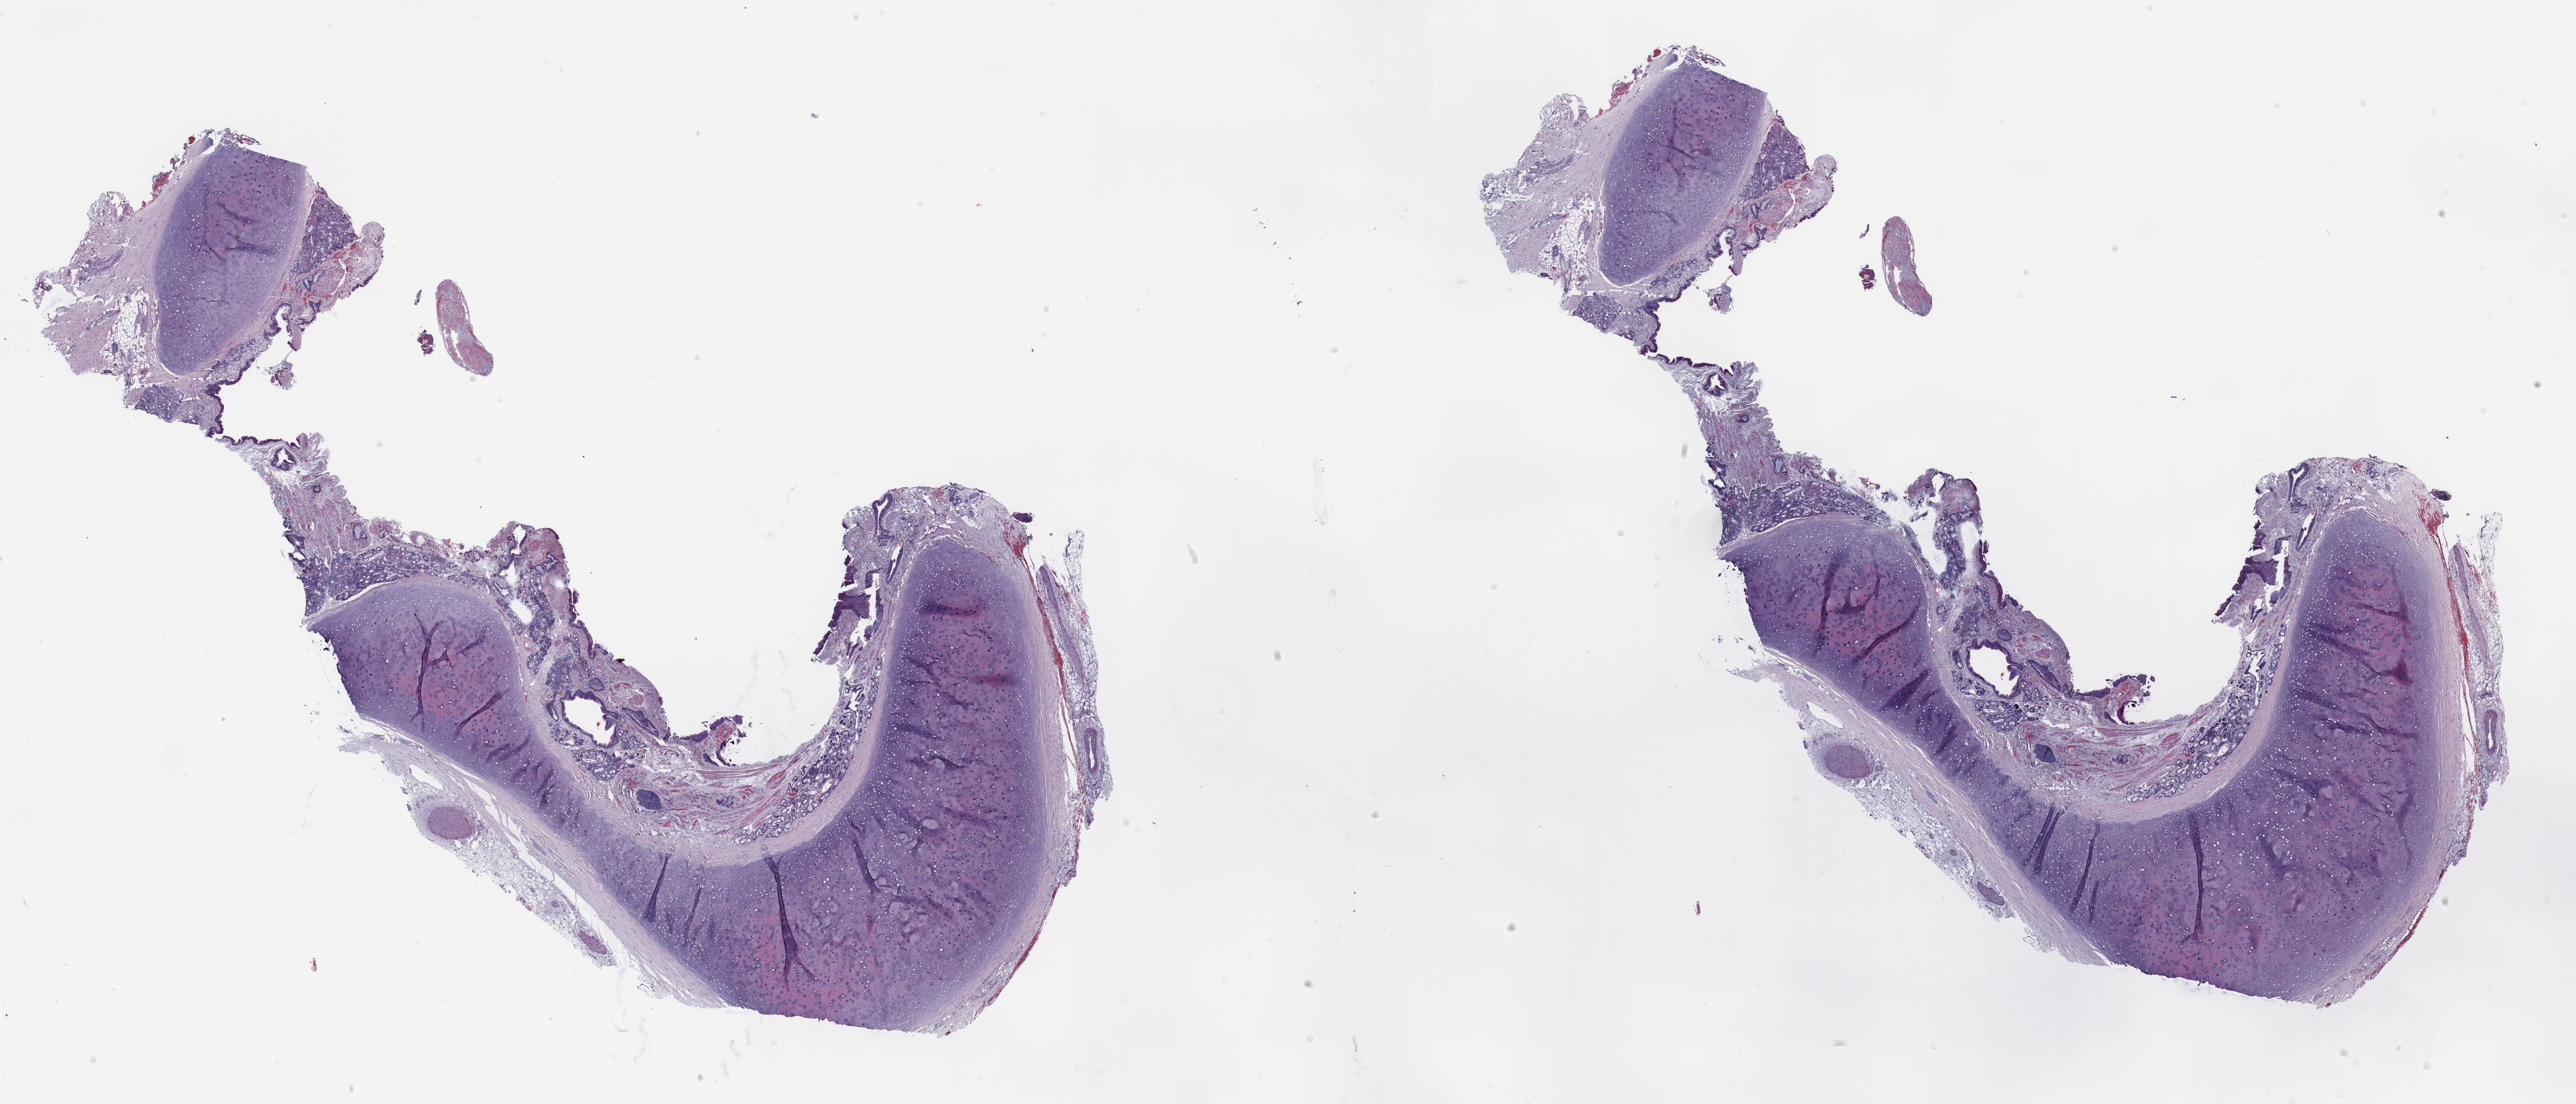
H&E whole-slide image — a low-resolution overview of the entire scanned area, about 37.0 x 15.9 mm; formalin-fixed paraffin-embedded (FFPE) section; lung. Male patient, aged 55 at enrolment. Current smoker at enrolment. Grade: poorly differentiated (G3).
- tumour size (pathology): 115 mm
- stage (AJCC 6th edition): IIB
- primary tumour location (clinical record): right upper lobe
- participant's lung-cancer diagnosis: Adenocarcinoma, NOS (ICD-O-3 8140/3)